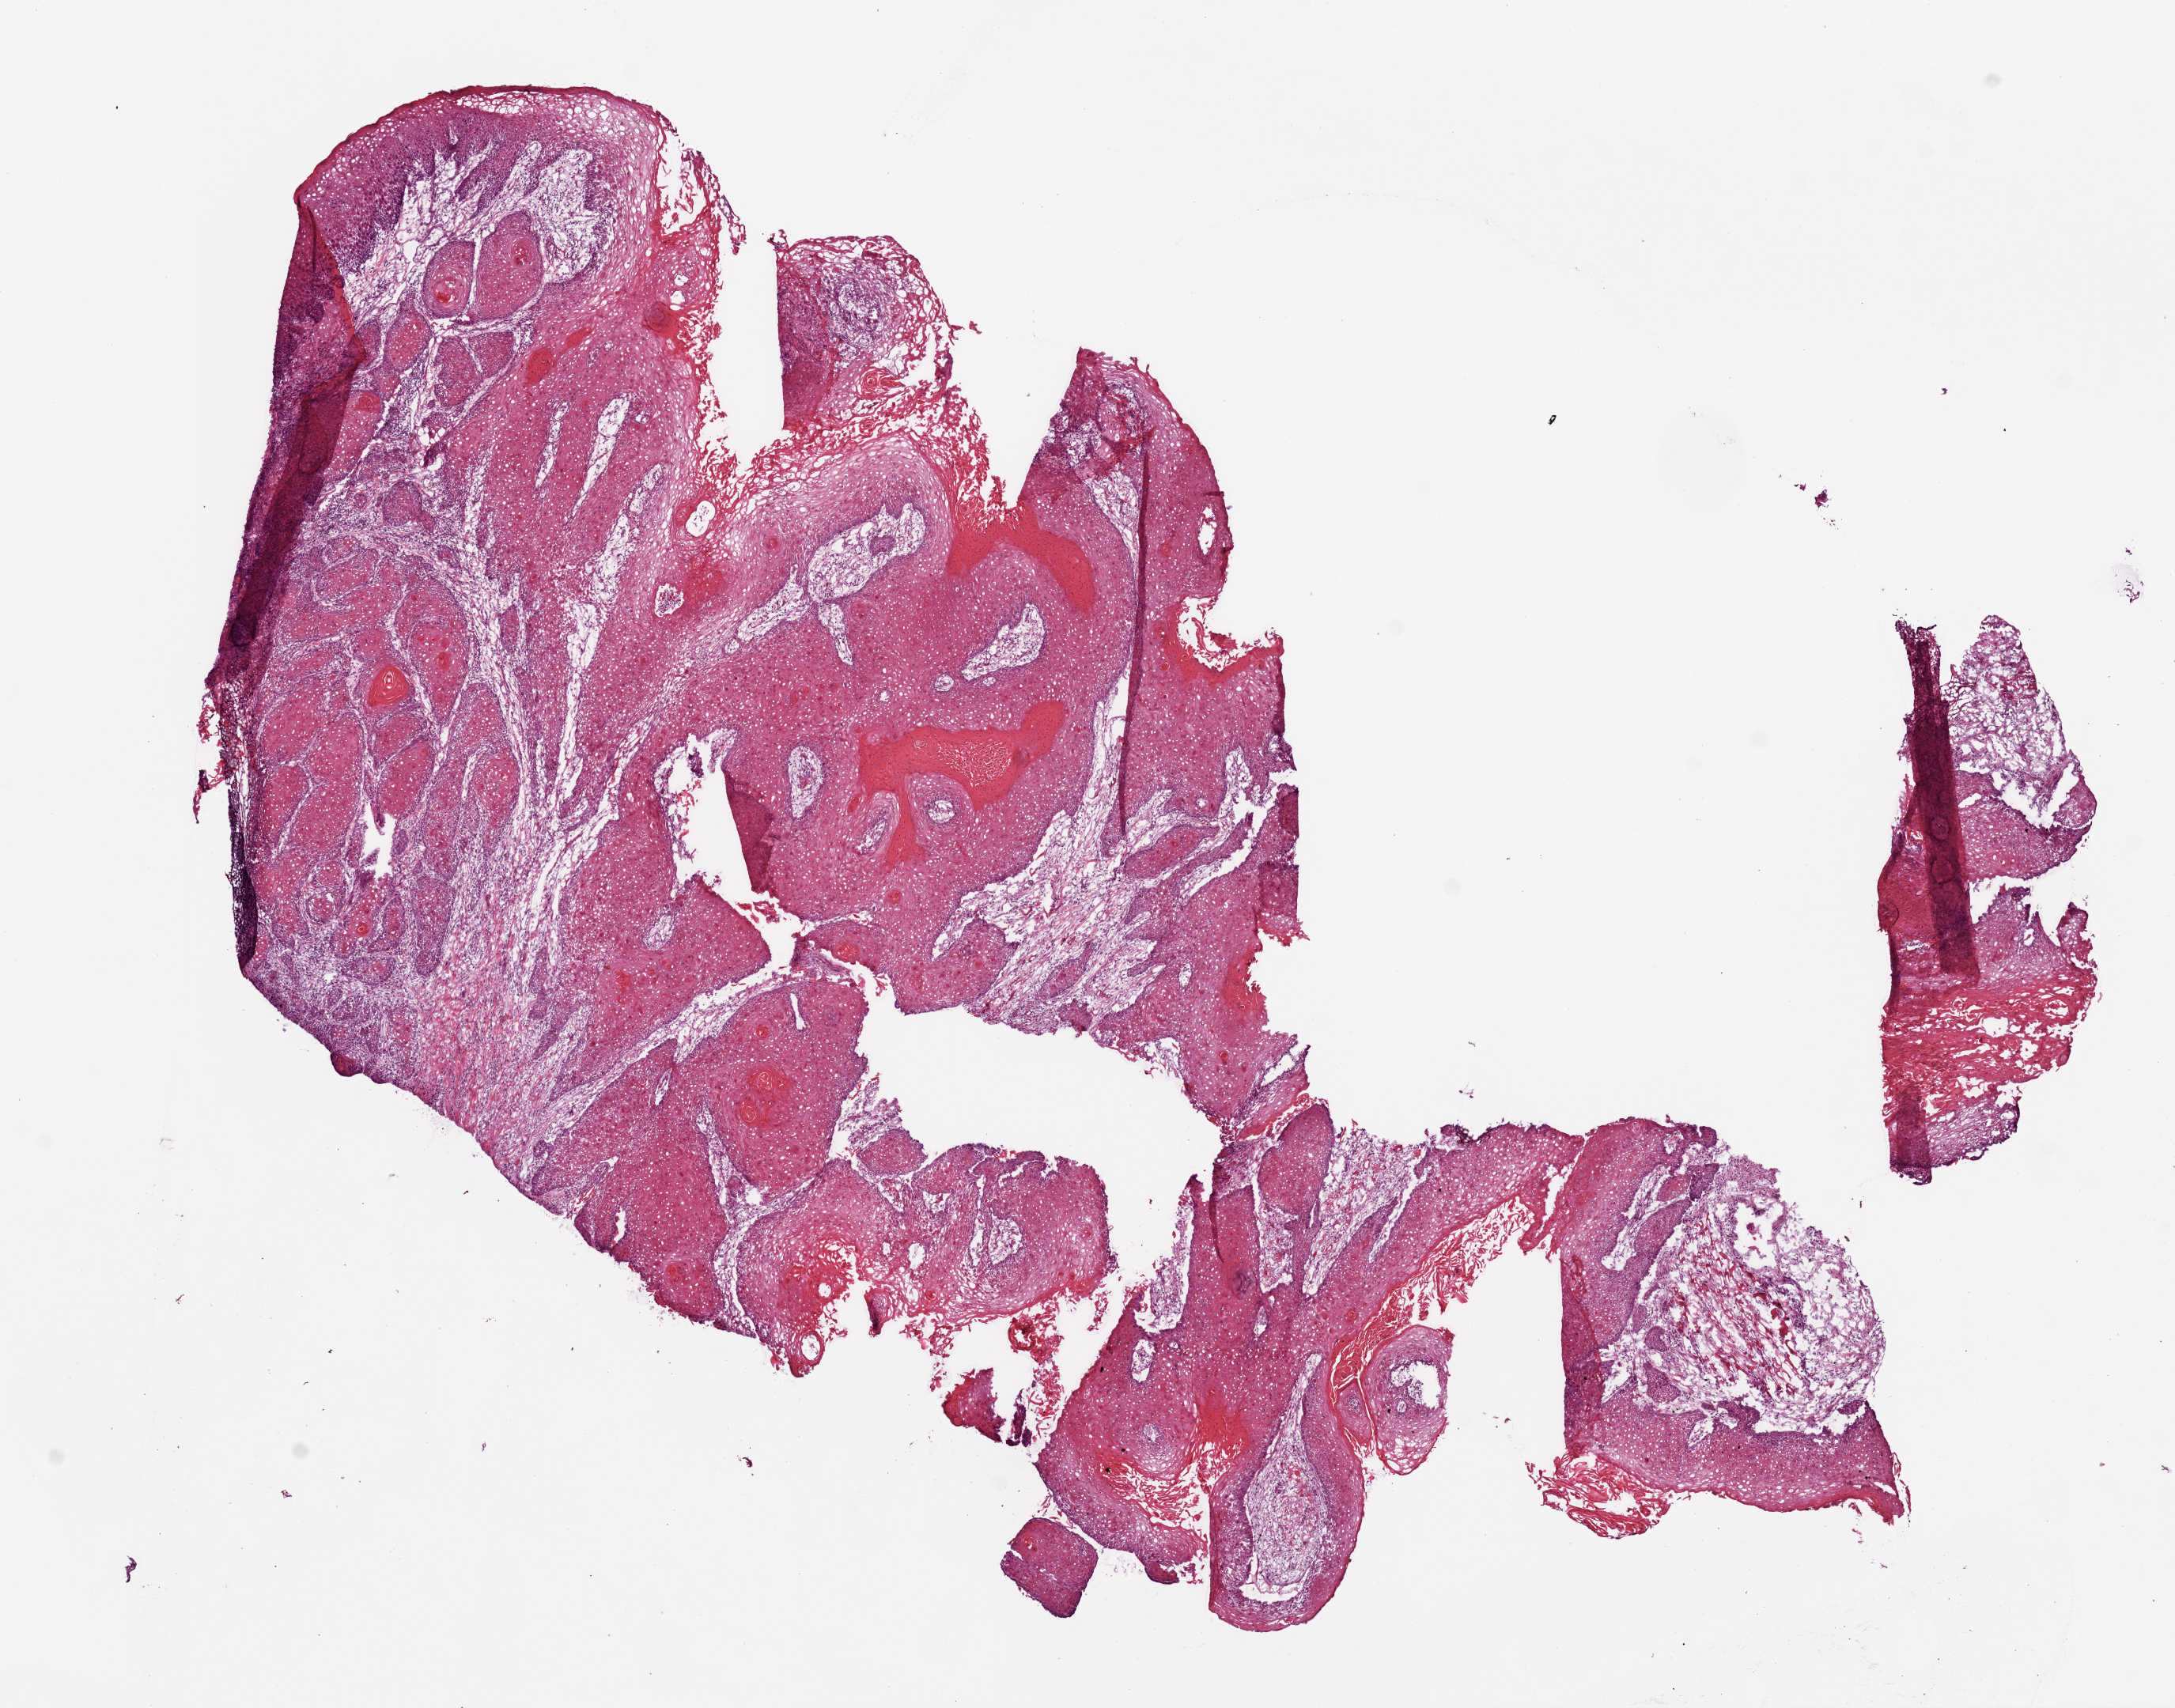
Whole-slide histology image, H&E-stained, whole scanned area (about 11.0 x 8.7 mm) shown as a low-resolution overview, frozen section, sample: primary tumour, head and neck. Female patient; age at initial diagnosis 55 years. Histologic grade: G1 (well differentiated). Slide review estimates, as recorded: tumour cells 75%, tumour nuclei 75%, normal cells 10%, stromal cells 15%, necrosis 0%.
• AJCC pathologic stage: I (7th edition)
• histologic diagnosis: Squamous cell carcinoma, NOS (floor of mouth, NOS)